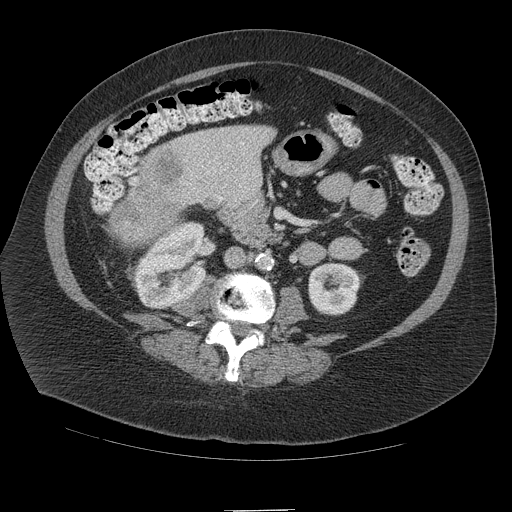
Contrast-enhanced abdominal CT (liver protocol), one axial slice. Slice 31 of 109 in the series (ordered by position). 140 kVp. Soft-tissue window (W 400 / L 40 HU). 2.5 mm slice thickness. 512 × 512 image matrix. From the clinical record (not read from this slice): diagnosis: hepatocellular carcinoma (patient treated with transarterial chemoembolisation; whether this scan precedes or follows treatment is not stated here); TNM stage (as recorded): Stage-IVB; Child-Pugh class: A.
Annotated regions visible in this slice (semi-automatically segmented with operator editing):
- liver parenchyma outside the tumour (the mass and vessels are separate outlines, so this box may not span the whole liver): bounding box [x1, y1, x2, y2] px = [120, 125, 274, 210]
- mass: [109, 150, 183, 241]
- liver vessels: [207, 142, 245, 201]